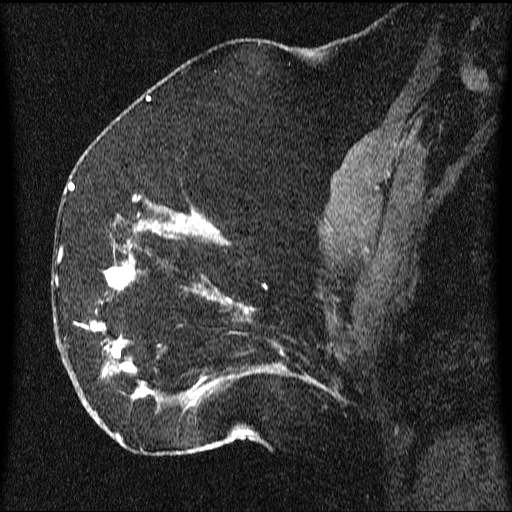
Breast MRI (dynamic contrast-enhanced), one sagittal slice; slice 26 of 64 in the series (ordered by position); dynamic contrast-enhanced series, image 2 of 3 at this slice position (ordered by acquisition); 1.5 T; TE 4.2 ms, TR 9.1 ms; 2.2 mm slice thickness; 512 × 512 image matrix. Female patient, age 52 years.
Outlined on this slice (semi-automatically segmented with operator editing):
- analysis volume of interest (the breast-tissue region the enhancement analysis was run in; not a lesion): bounding box <61,203,350,438> (left, top, right, bottom; pixels)
- tumour enhancement mask (voxels above the 70 % enhancement threshold inside the analysis volume of interest): <61,212,323,438>